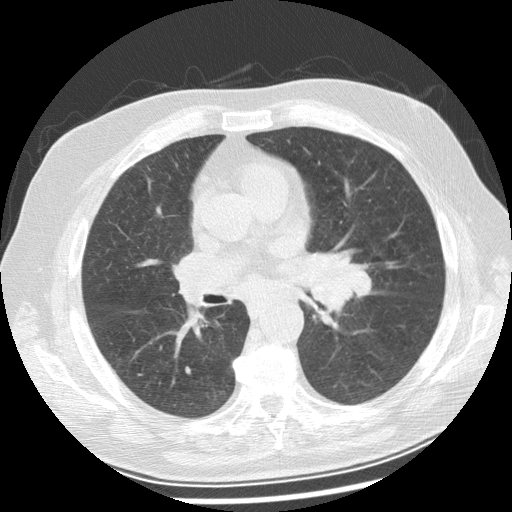
Chest CT (low-dose screening protocol), one axial image; baseline screening round; lung window (W 1500 / L -600 HU); 2.5 mm slice thickness. Male, age 70 years at enrolment. Current smoker at enrolment.
Expert reader's lesion annotation, bounding box [x1, y1, x2, y2] px = [287, 241, 370, 316]. Screening reader's record for this exam: no non-calcified nodule ≥4 mm recorded. Later outcome: lung cancer diagnosed 29 days after this screen — squamous cell carcinoma, keratinizing, NOS, left main stem bronchus, moderately differentiated (G2), stage IIIB (AJCC 6th edition), 40 mm at pathology.